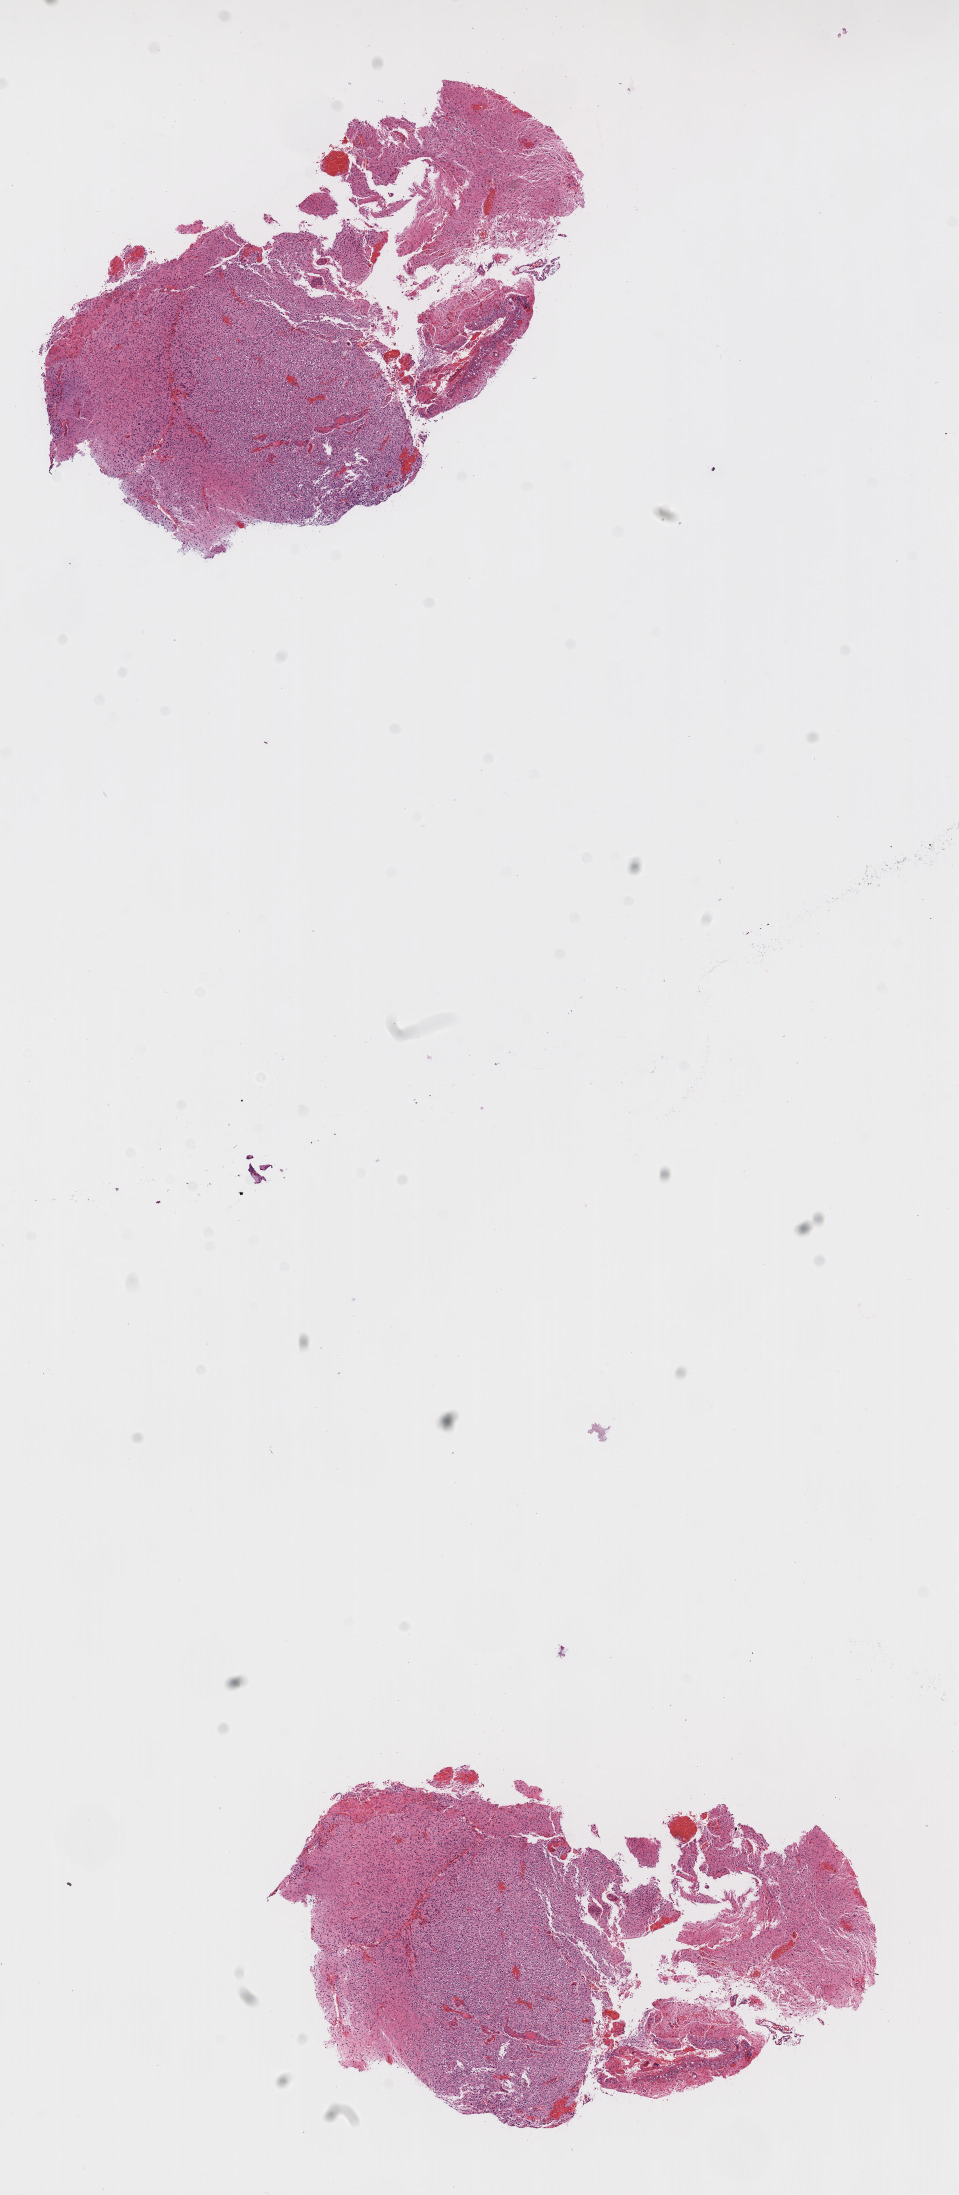
Digitized H&E-stained tissue section (whole slide), a low-resolution overview of the entire scanned area, about 7.7 x 17.7 mm, FFPE section, primary tumour sample from the brain. Patient: male, age at initial diagnosis 66 years.
Diagnosis: Glioblastoma.